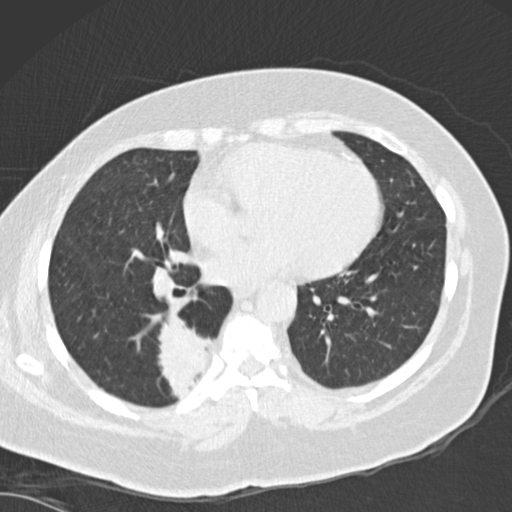
Chest CT (low-dose screening protocol), one axial image; baseline screening round; lung window (W 1500 / L -600 HU); slice 95 of 162 in the series. Female, age 66 years at enrolment.
Lesion marked by an expert reader, box from (x=150, y=321) to (x=226, y=399) px. The screening reader recorded 3 non-calcified nodules or masses ≥4 mm on this exam; which of them this box marks is not recorded. Participant outcome: lung cancer diagnosed 67 days after this screen — adenocarcinoma, NOS, right lower lobe, well differentiated (G1), stage IB (AJCC 6th edition), 55 mm at pathology.